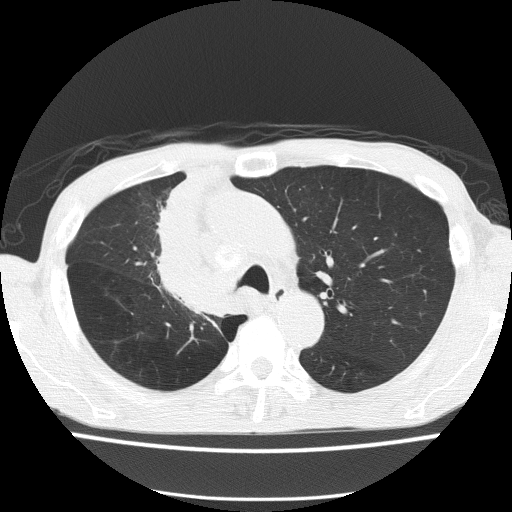
Axial slice from a low-dose chest CT screening exam. First (baseline) screen. Lung window (W 1500 / L -600 HU). 2 mm slice thickness. 120 kVp. Slice 47 of 150 in the series. Male participant, aged 59 years at enrolment. Former smoker at enrolment.
- Expert-annotated lung lesion, box from (x=137, y=232) to (x=235, y=324) px.
- The screening reader recorded 5 non-calcified nodules or masses ≥4 mm on this exam (left upper lobe, left upper lobe, left upper lobe, right middle lobe, right lower lobe); which of them this box marks is not recorded.